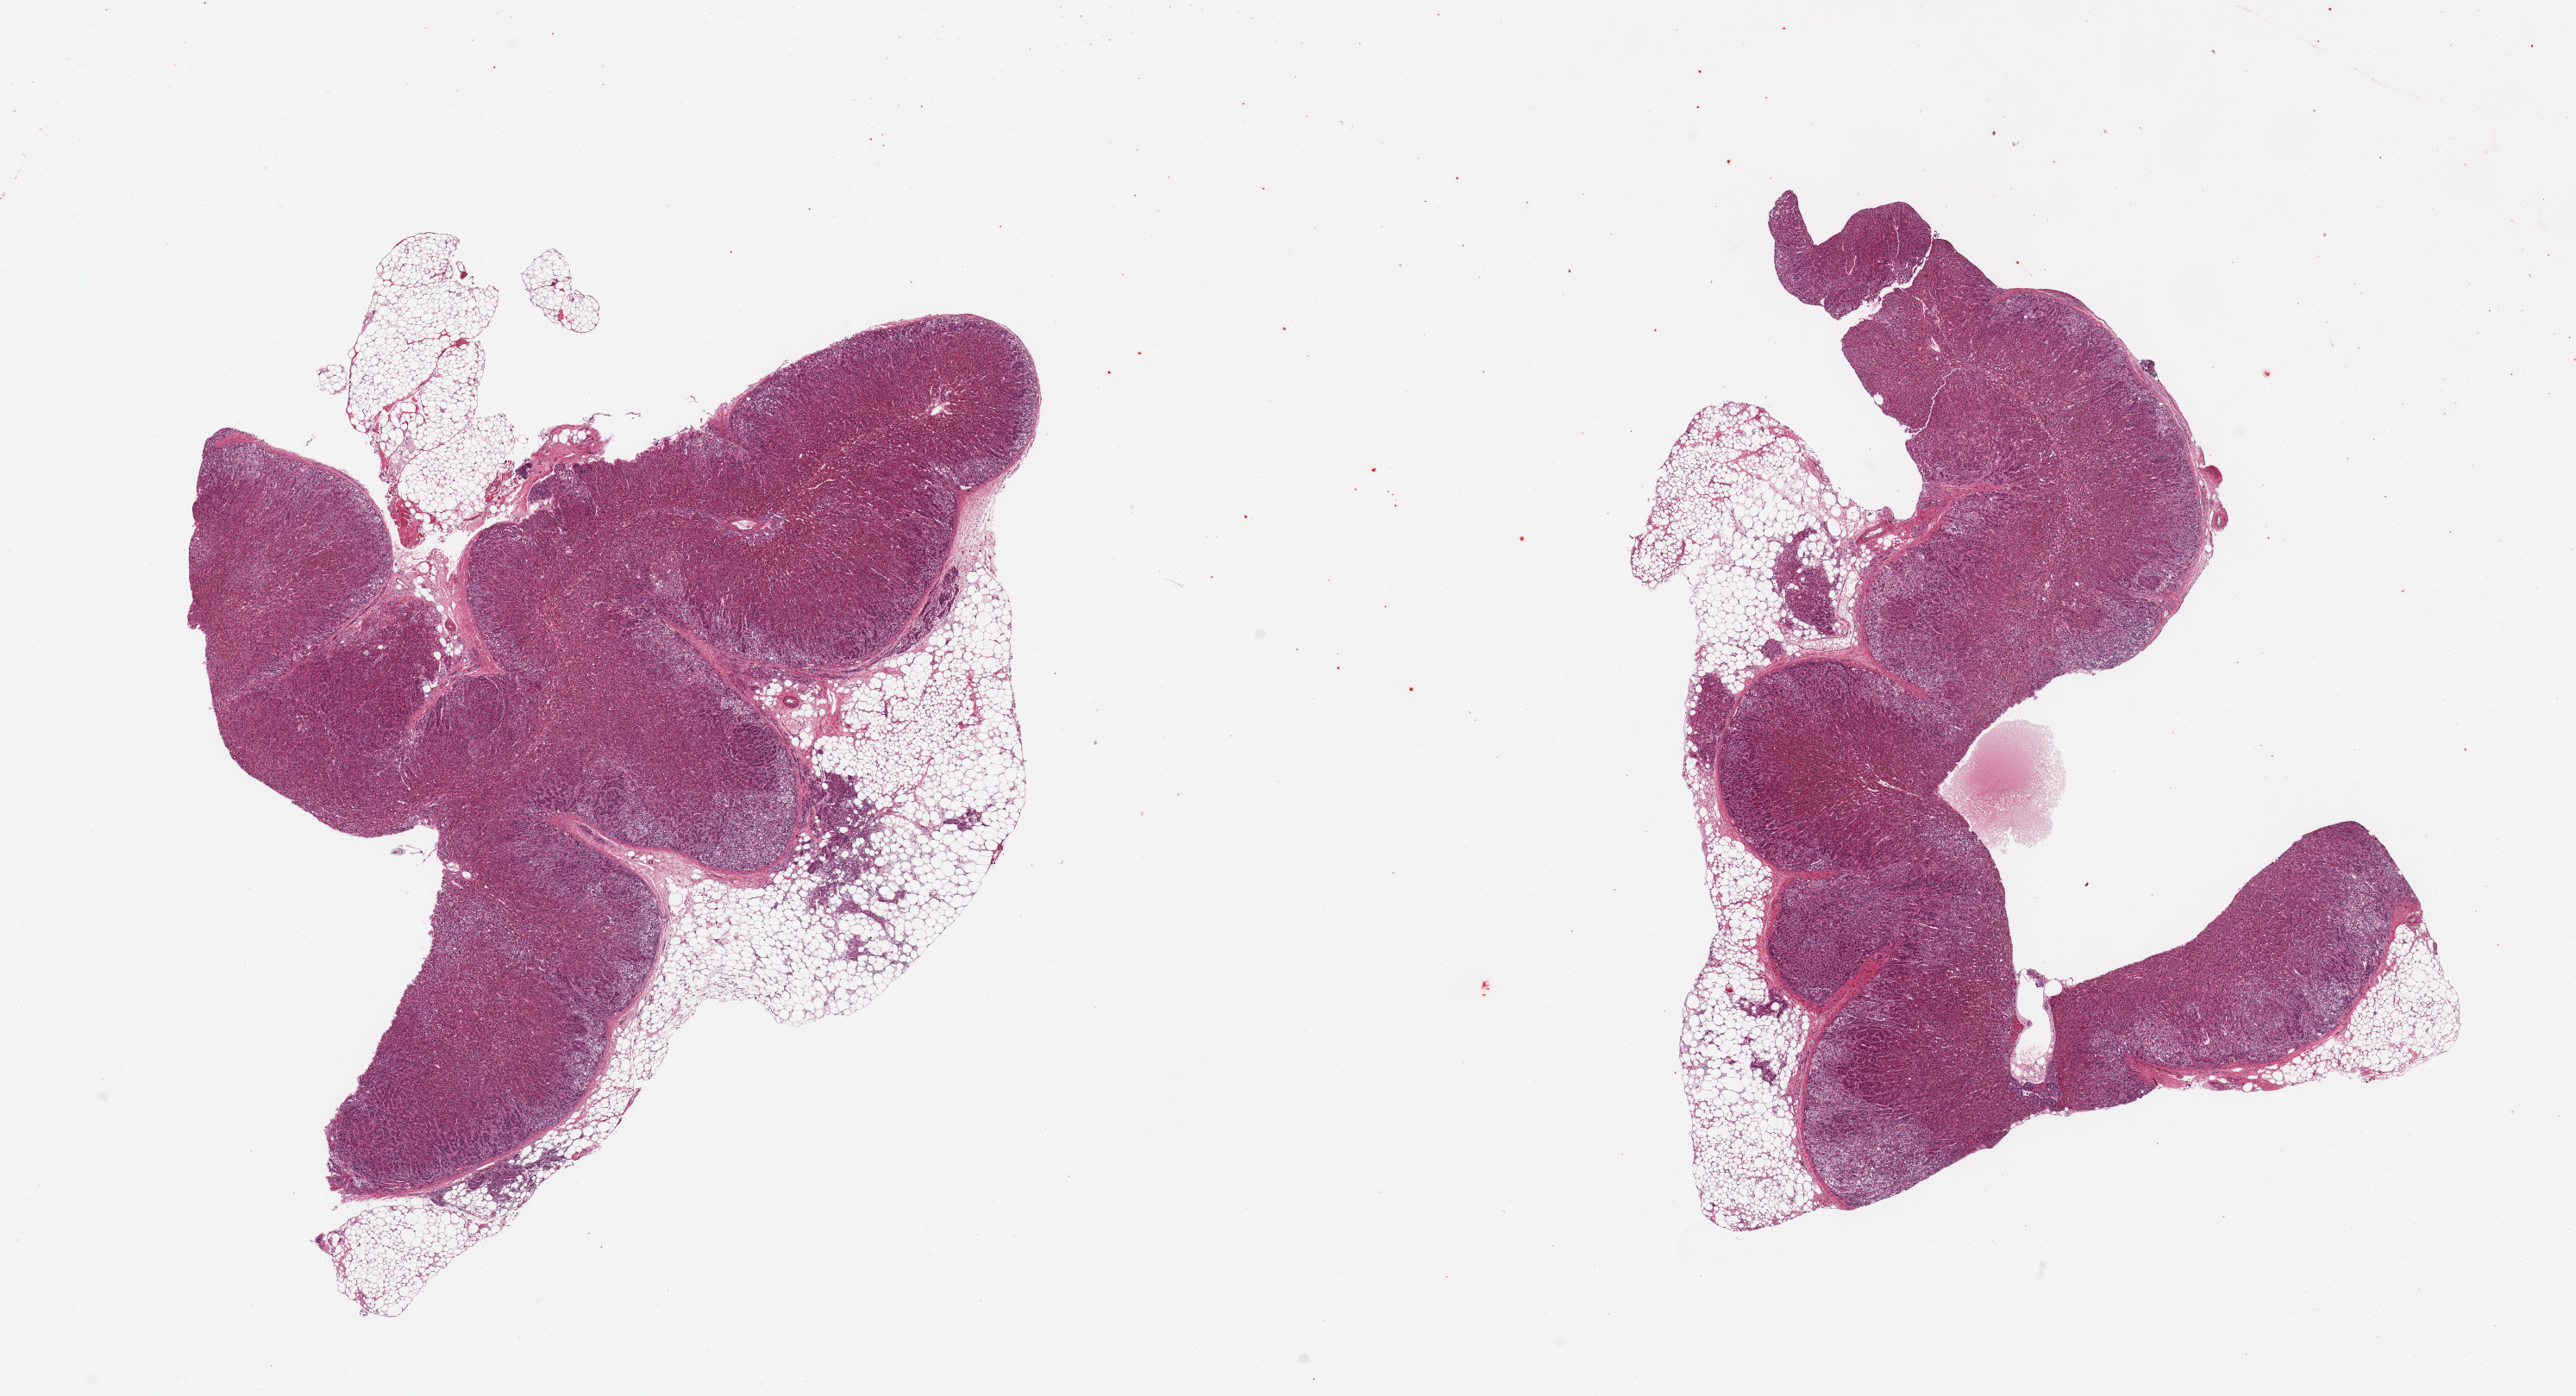
Digitized hematoxylin and eosin (H&E)-stained section, shown as a low-resolution overview of the whole scanned area (about 23.6 x 12.8 mm, from a 20x scan); PAXgene-fixed paraffin-embedded (PFPE) section; sampled site (target tissue): adrenal gland; tissue donor sample.
Reviewer comment on this tissue sample: 2 pieces; 40% external fat.